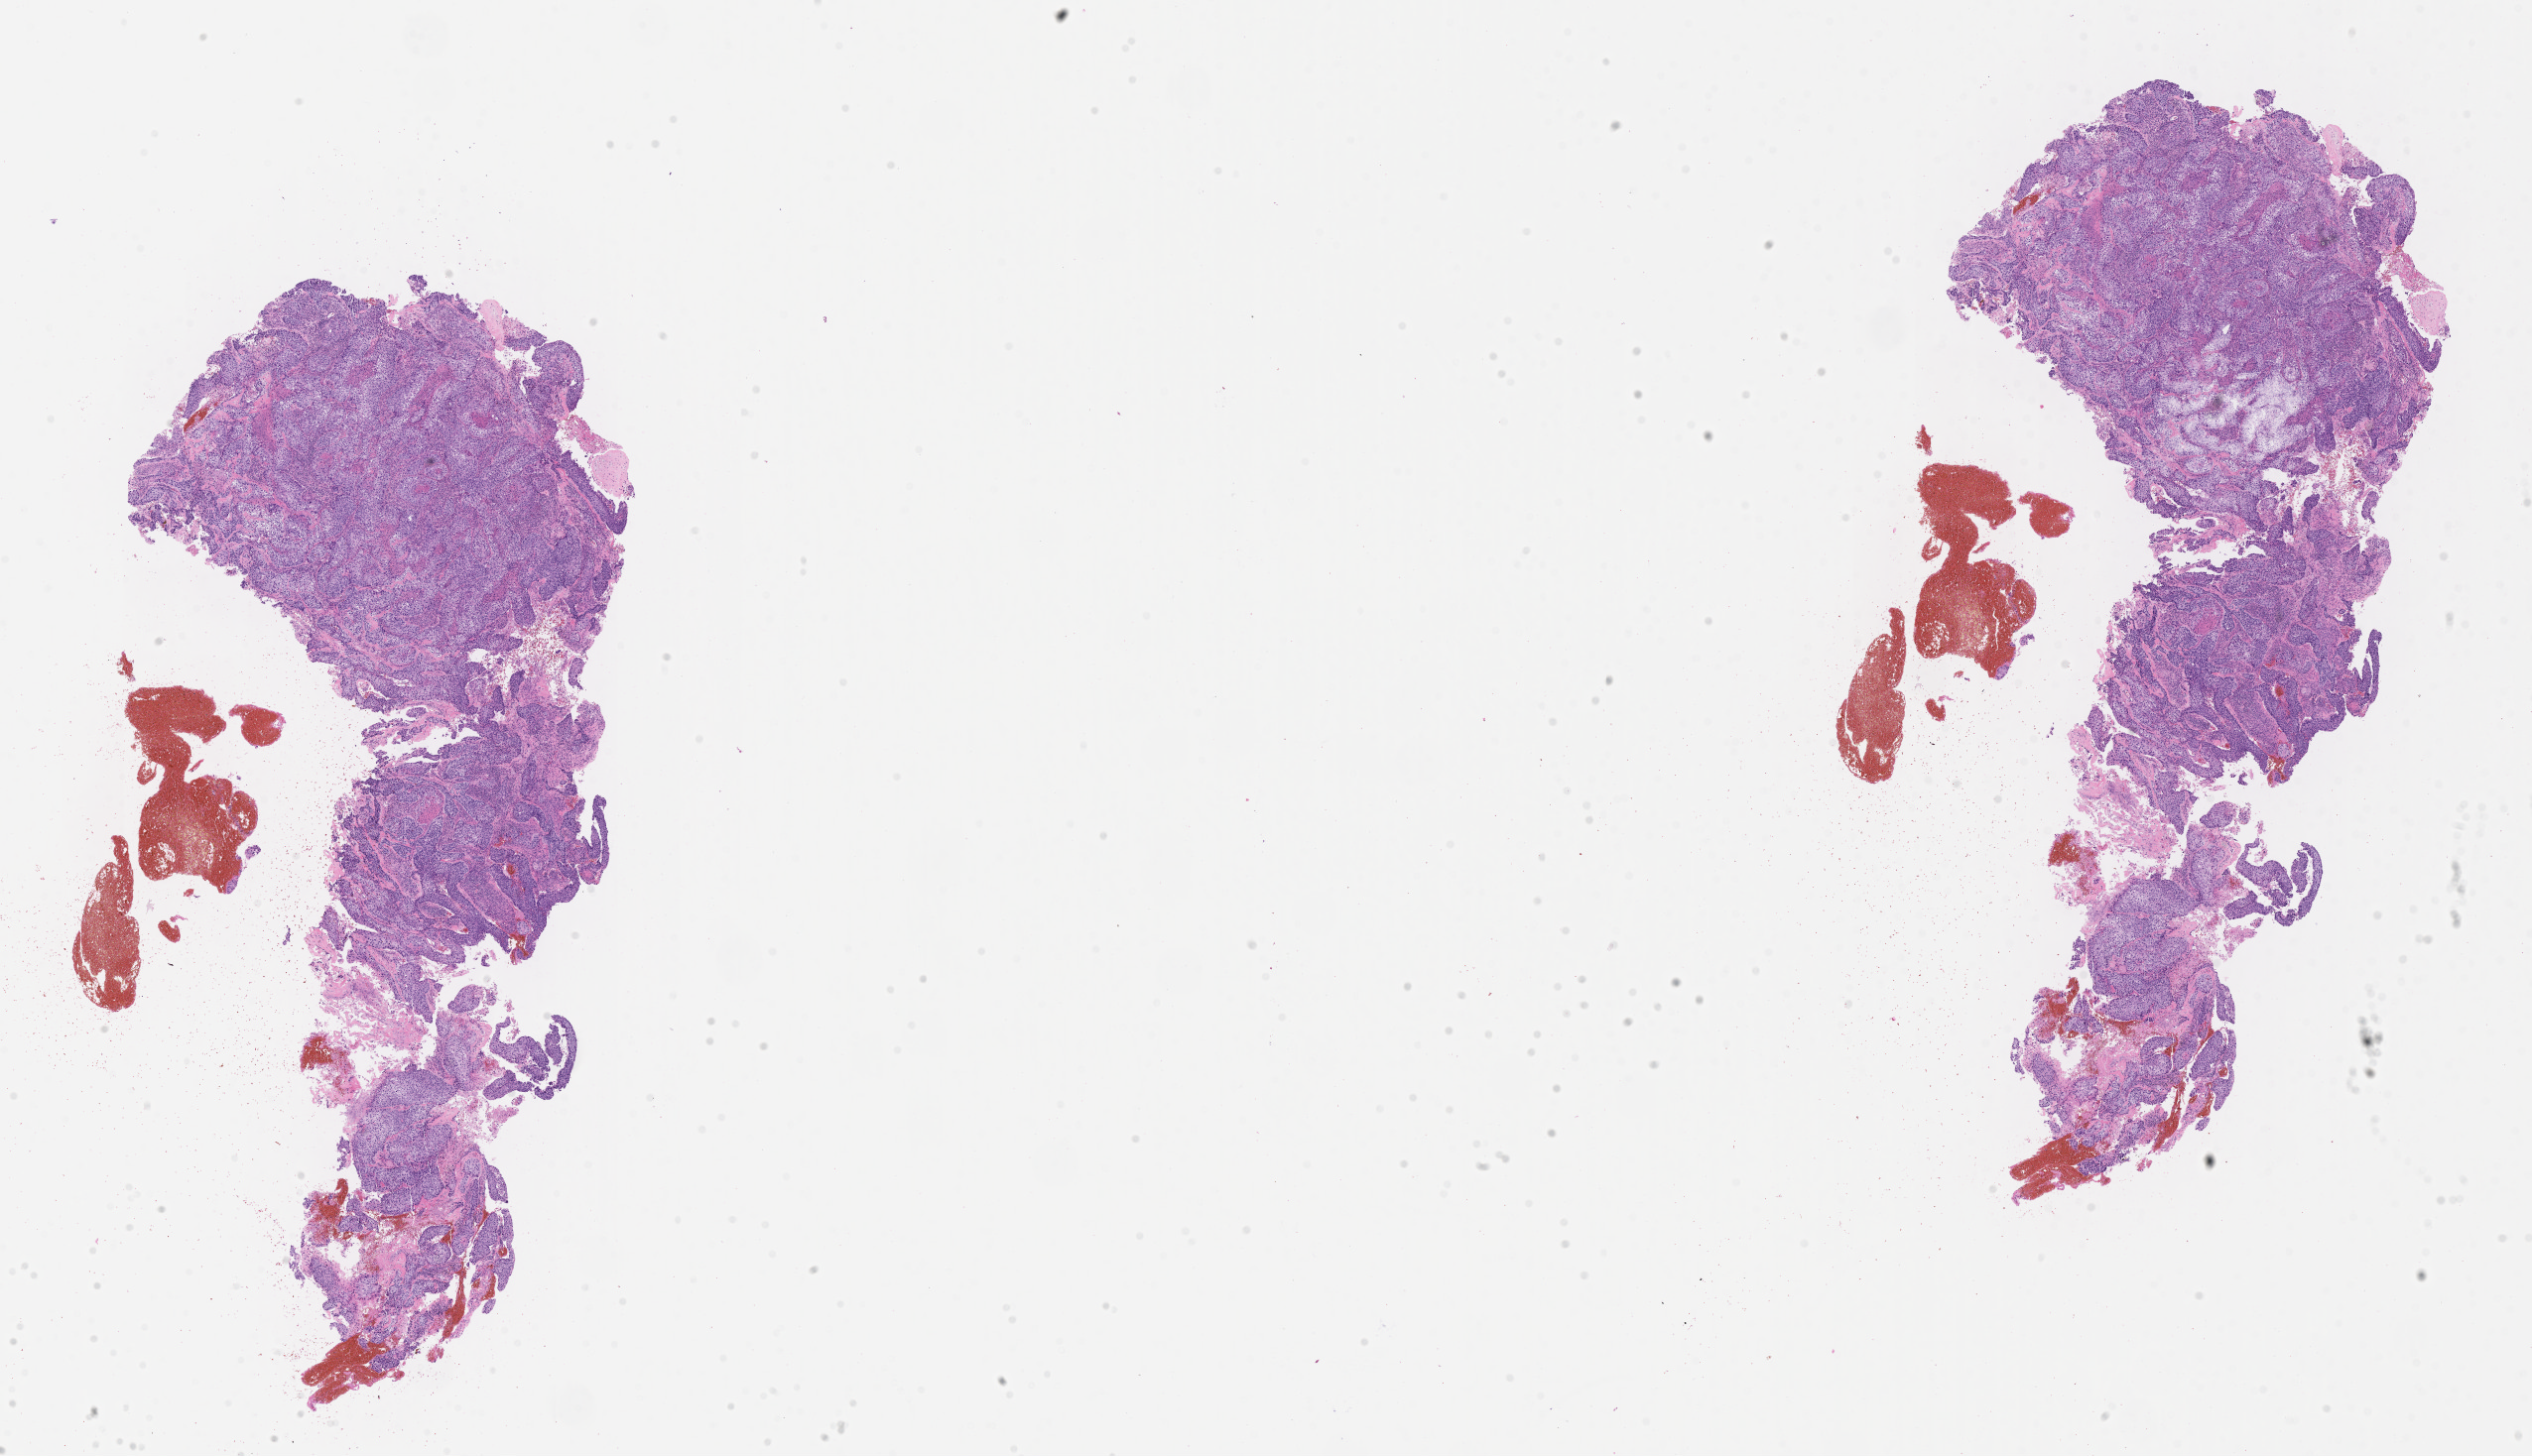
Digitized H&E-stained section, a low-resolution overview of the entire scanned area, about 20.6 x 11.9 mm, tumor tissue, site: cervix. Patient: female, aged 53.
Histologic diagnosis: Squamous cell carcinoma, keratinizing, NOS.